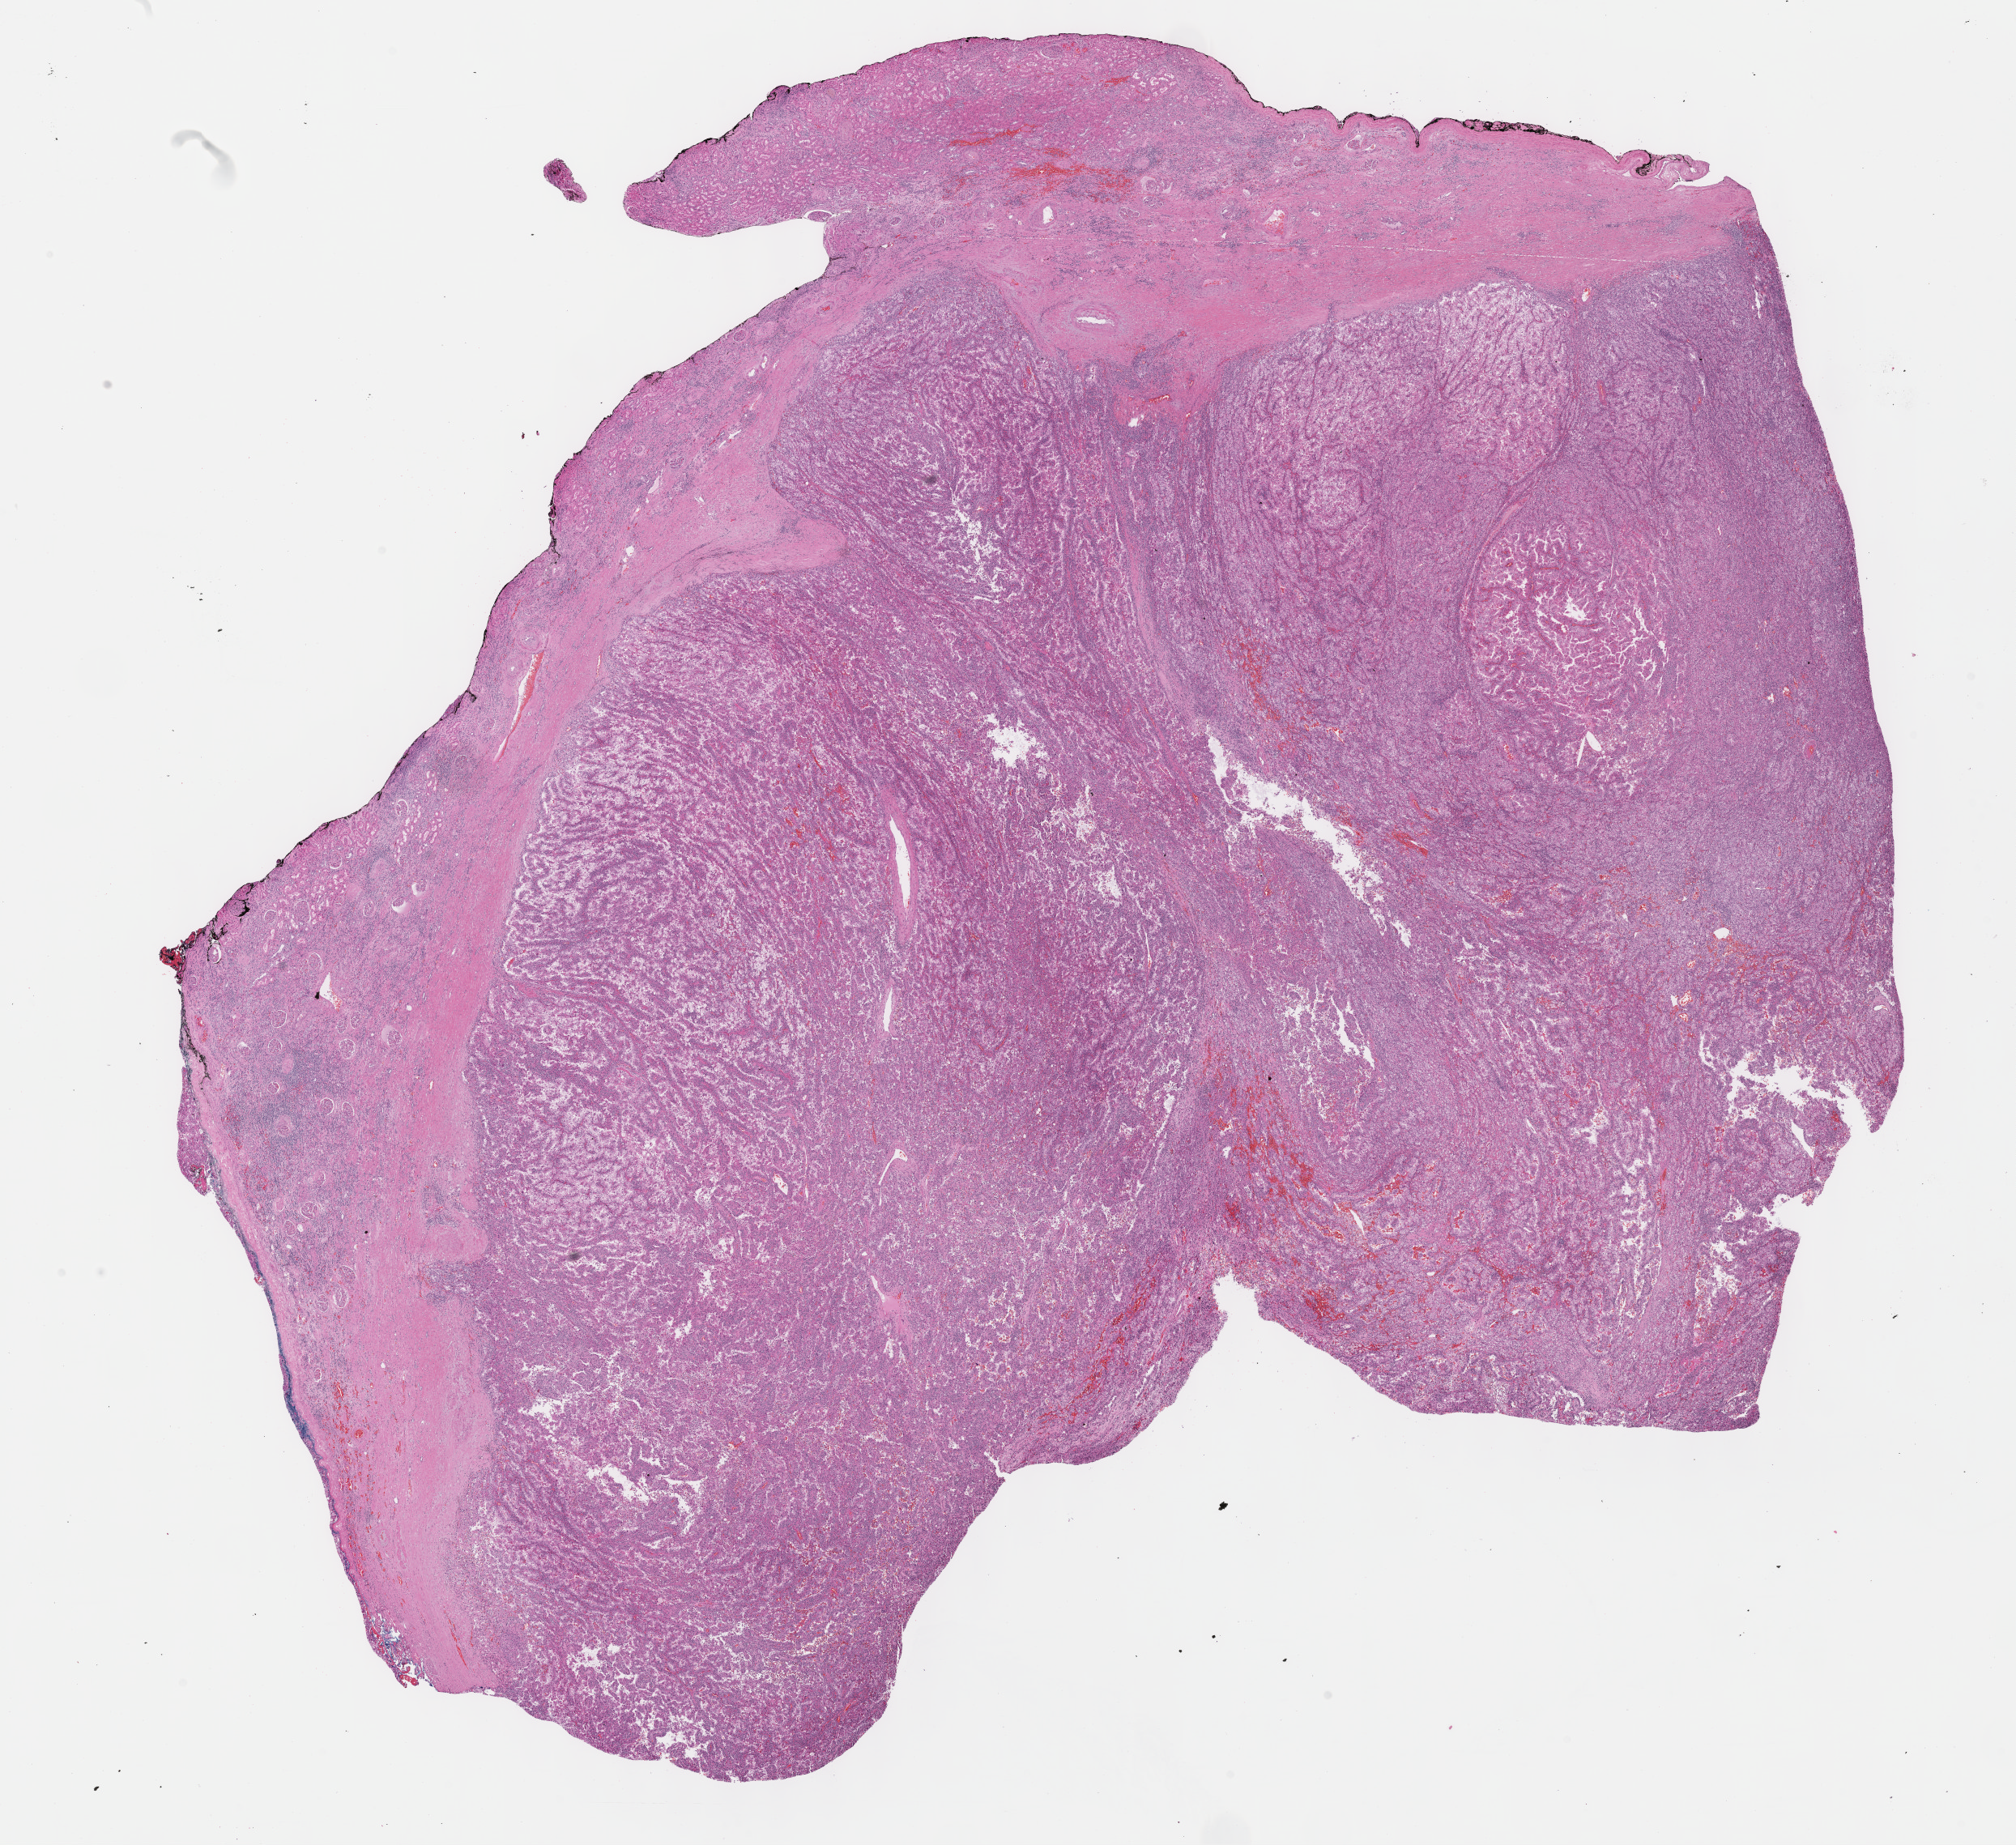
H&E-stained whole-slide image, whole scanned area (about 20.1 x 18.4 mm, acquisition: 40x scan) shown as a low-resolution overview. Formalin-fixed paraffin-embedded (FFPE) diagnostic section. Primary tumour sample from the kidney. Male patient; age at initial diagnosis 55 years.
• diagnosis: Papillary adenocarcinoma, NOS
• AJCC pathologic stage: I (7th edition)